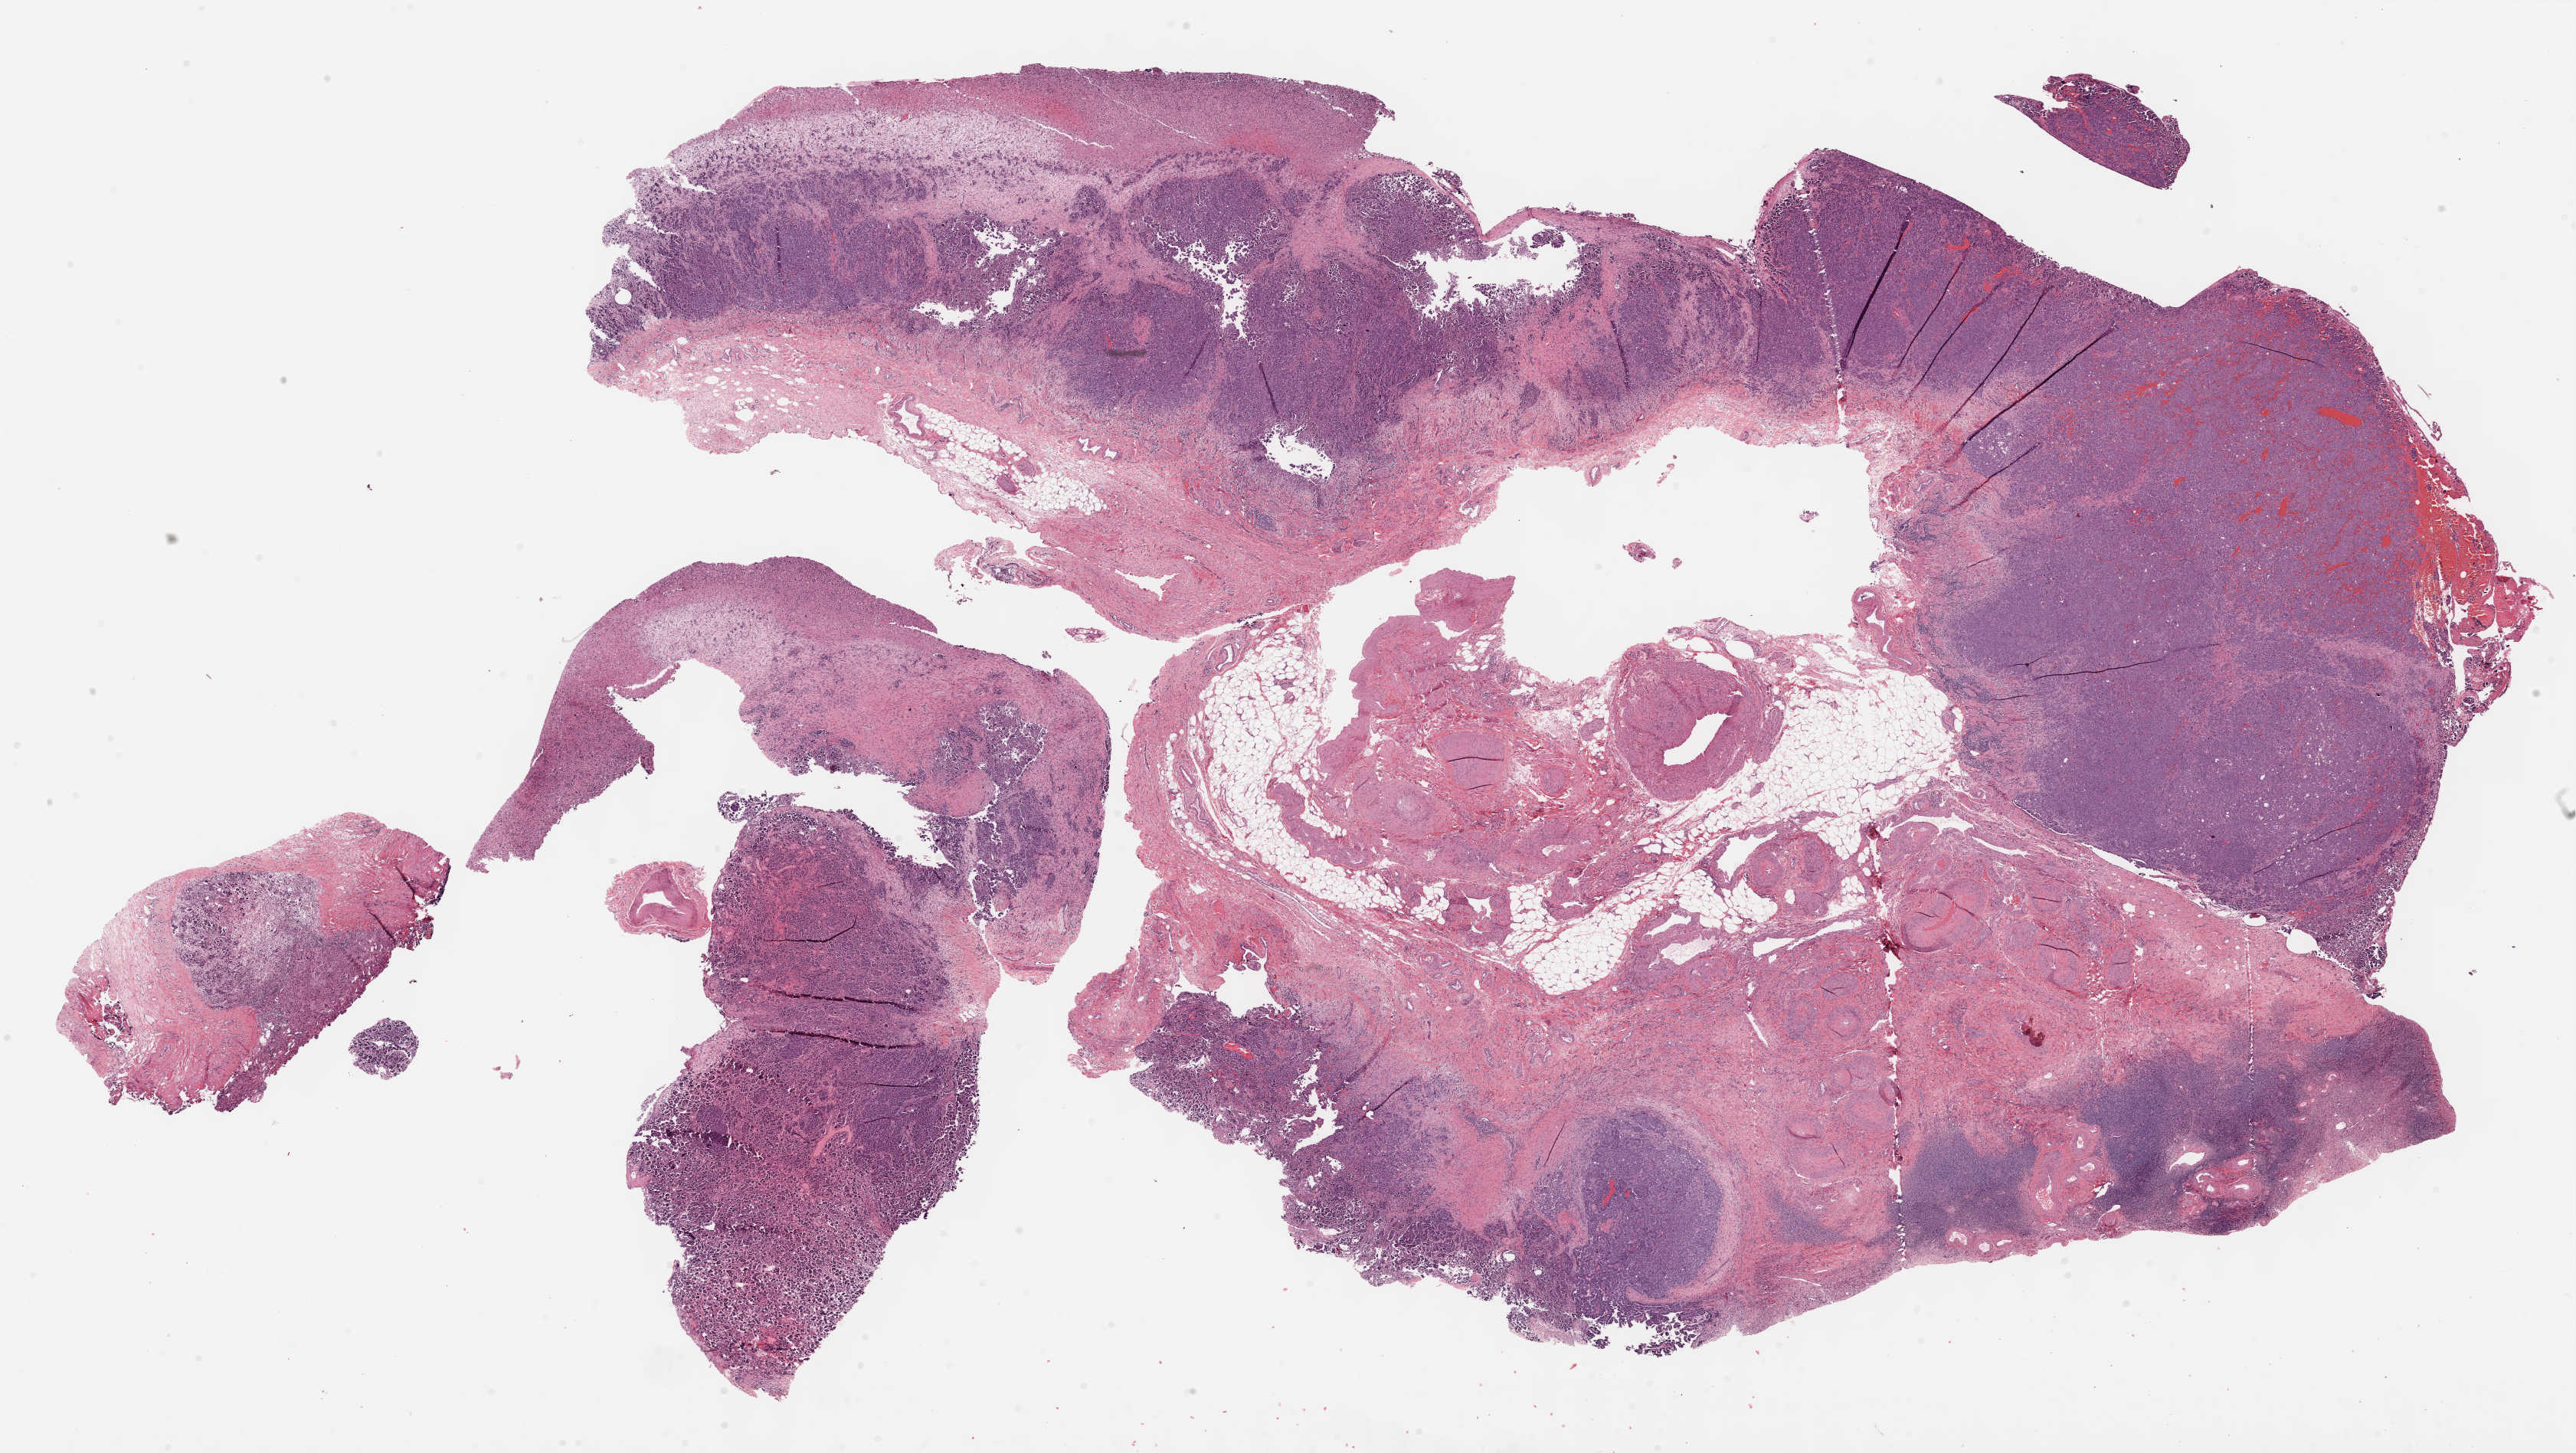
Digitized H&E-stained tissue section (whole slide), whole scanned area (about 27.2 x 15.3 mm, slide scanned at 40x) shown as a low-resolution overview; formalin-fixed paraffin-embedded (FFPE) diagnostic section; ovary, primary tumour sample. Female, age 64 years at initial diagnosis.
Histologic diagnosis: Serous cystadenocarcinoma, NOS.